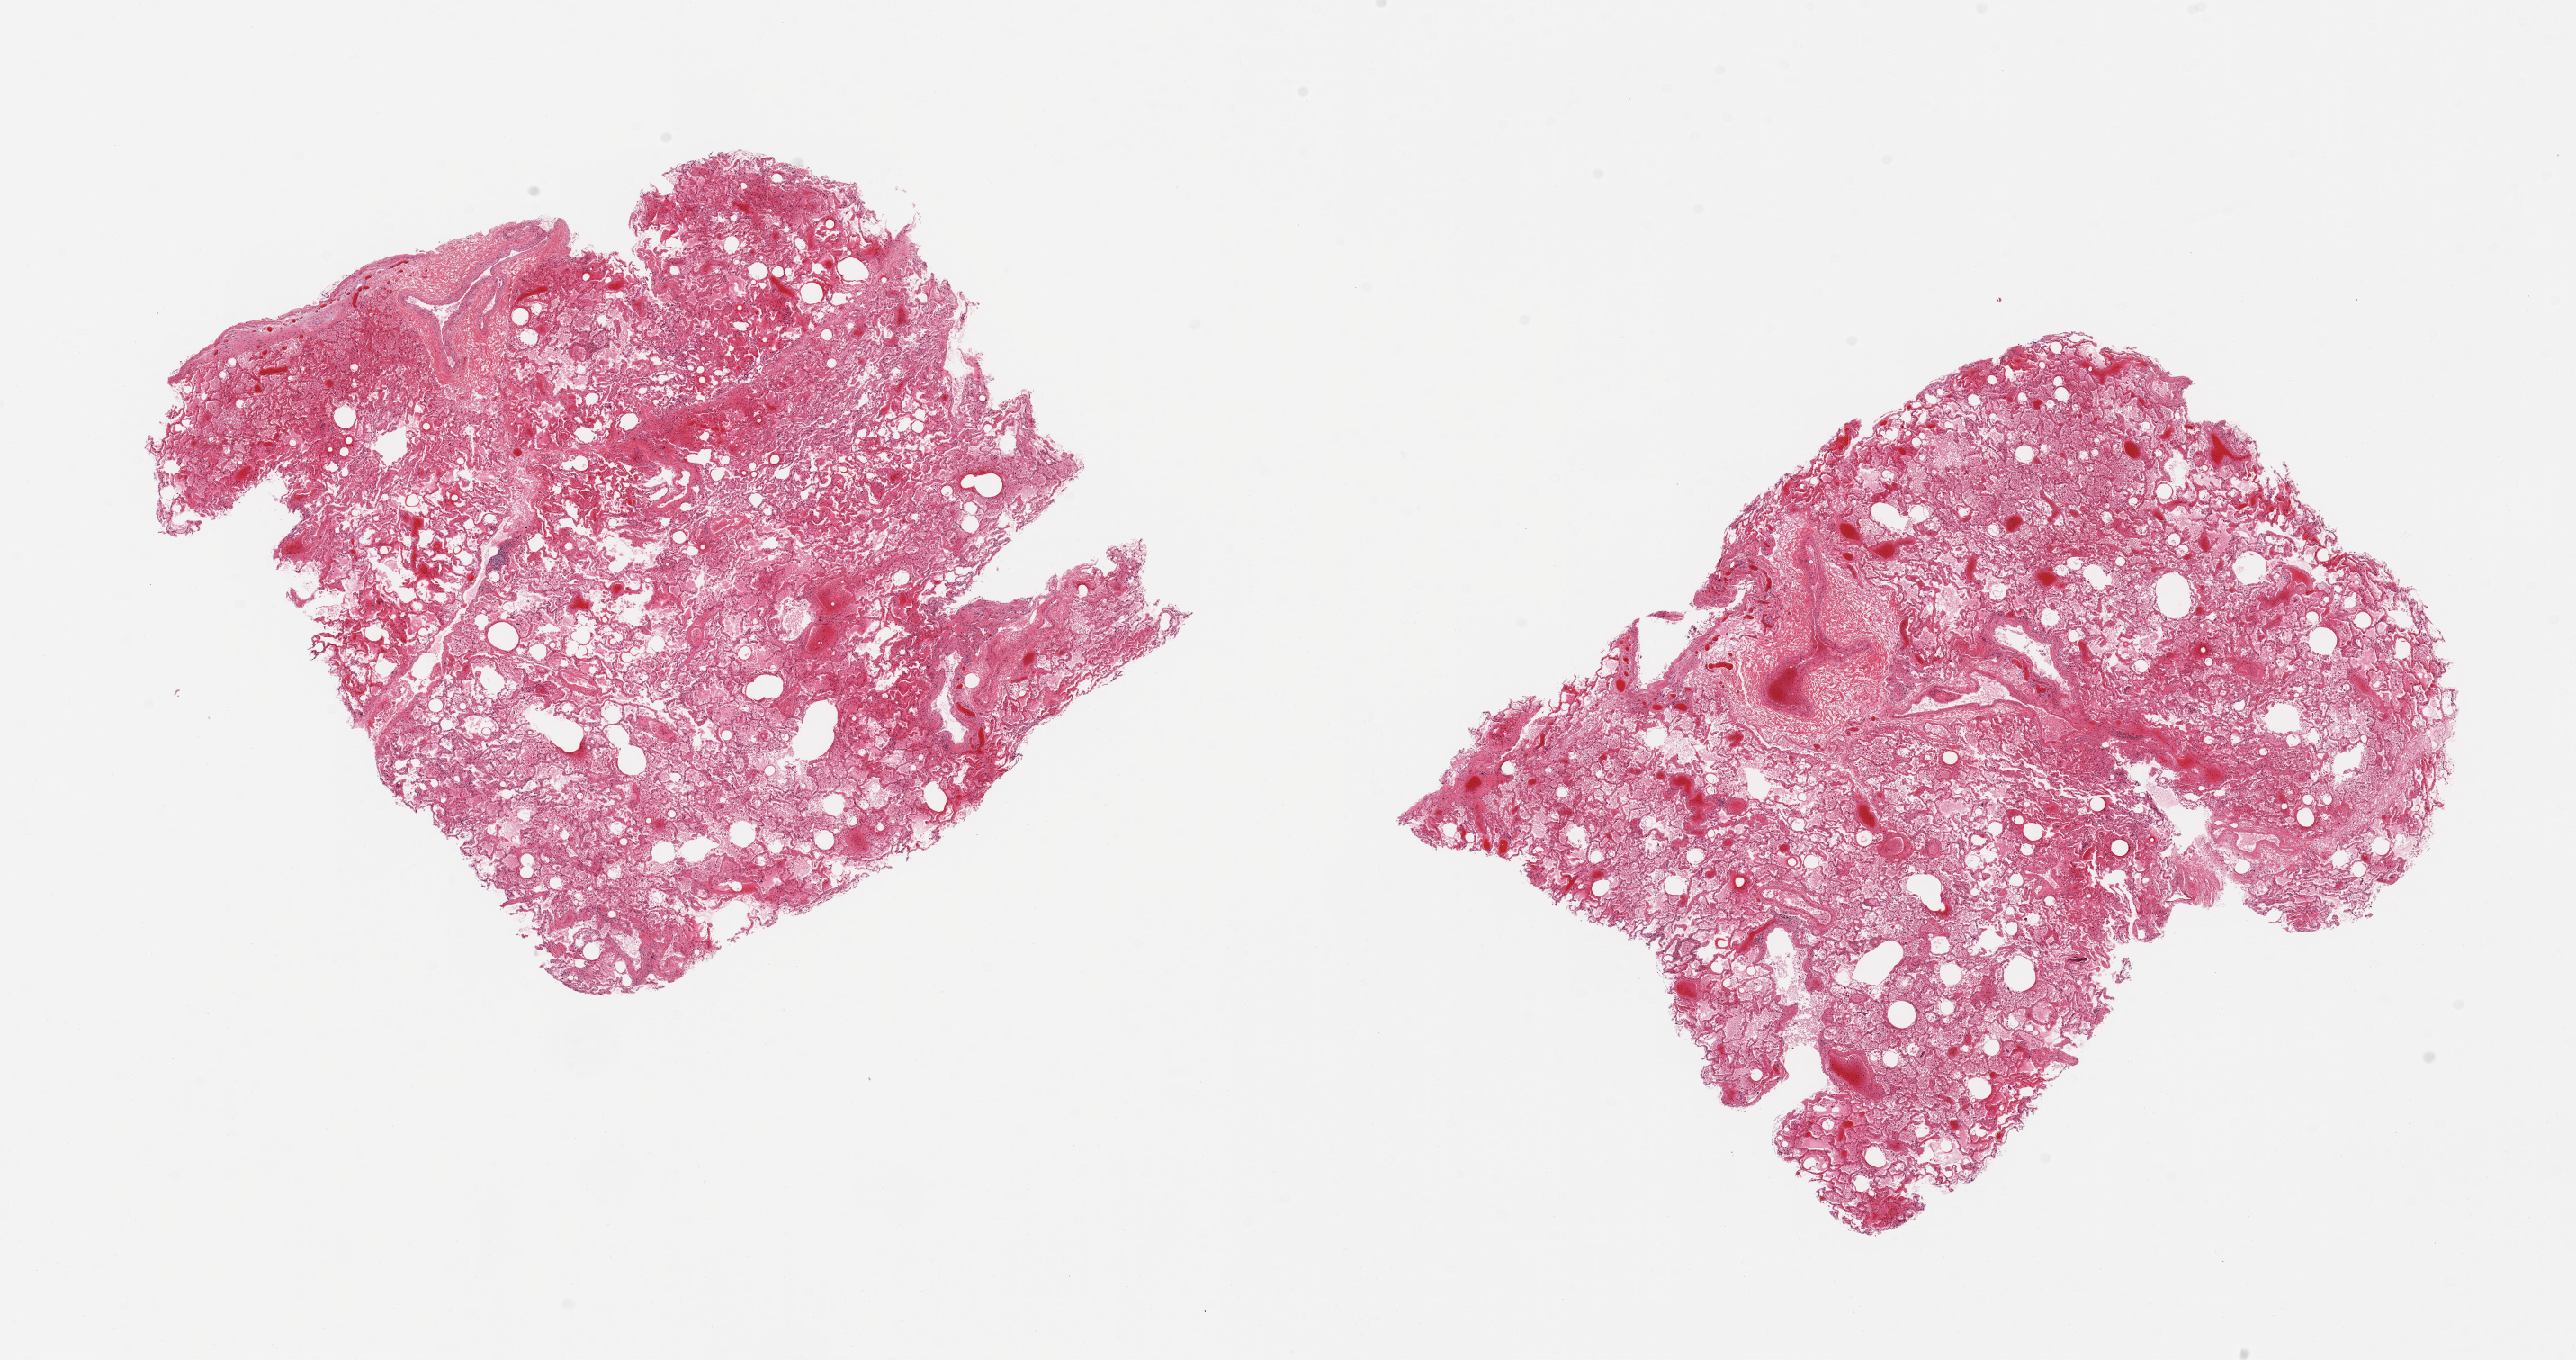
Hematoxylin and eosin (H&E) whole-slide image, brightfield — shown as a low-resolution overview of the whole scanned area (about 22.6 x 11.9 mm, slide scanned at 20x). PAXgene-fixed, paraffin-embedded tissue. Sampled site (target tissue): lung. Tissue donor sample. Donor sex: female.
• review note (as recorded): 2 pieces; moderate congestion and severe pulmonary edema